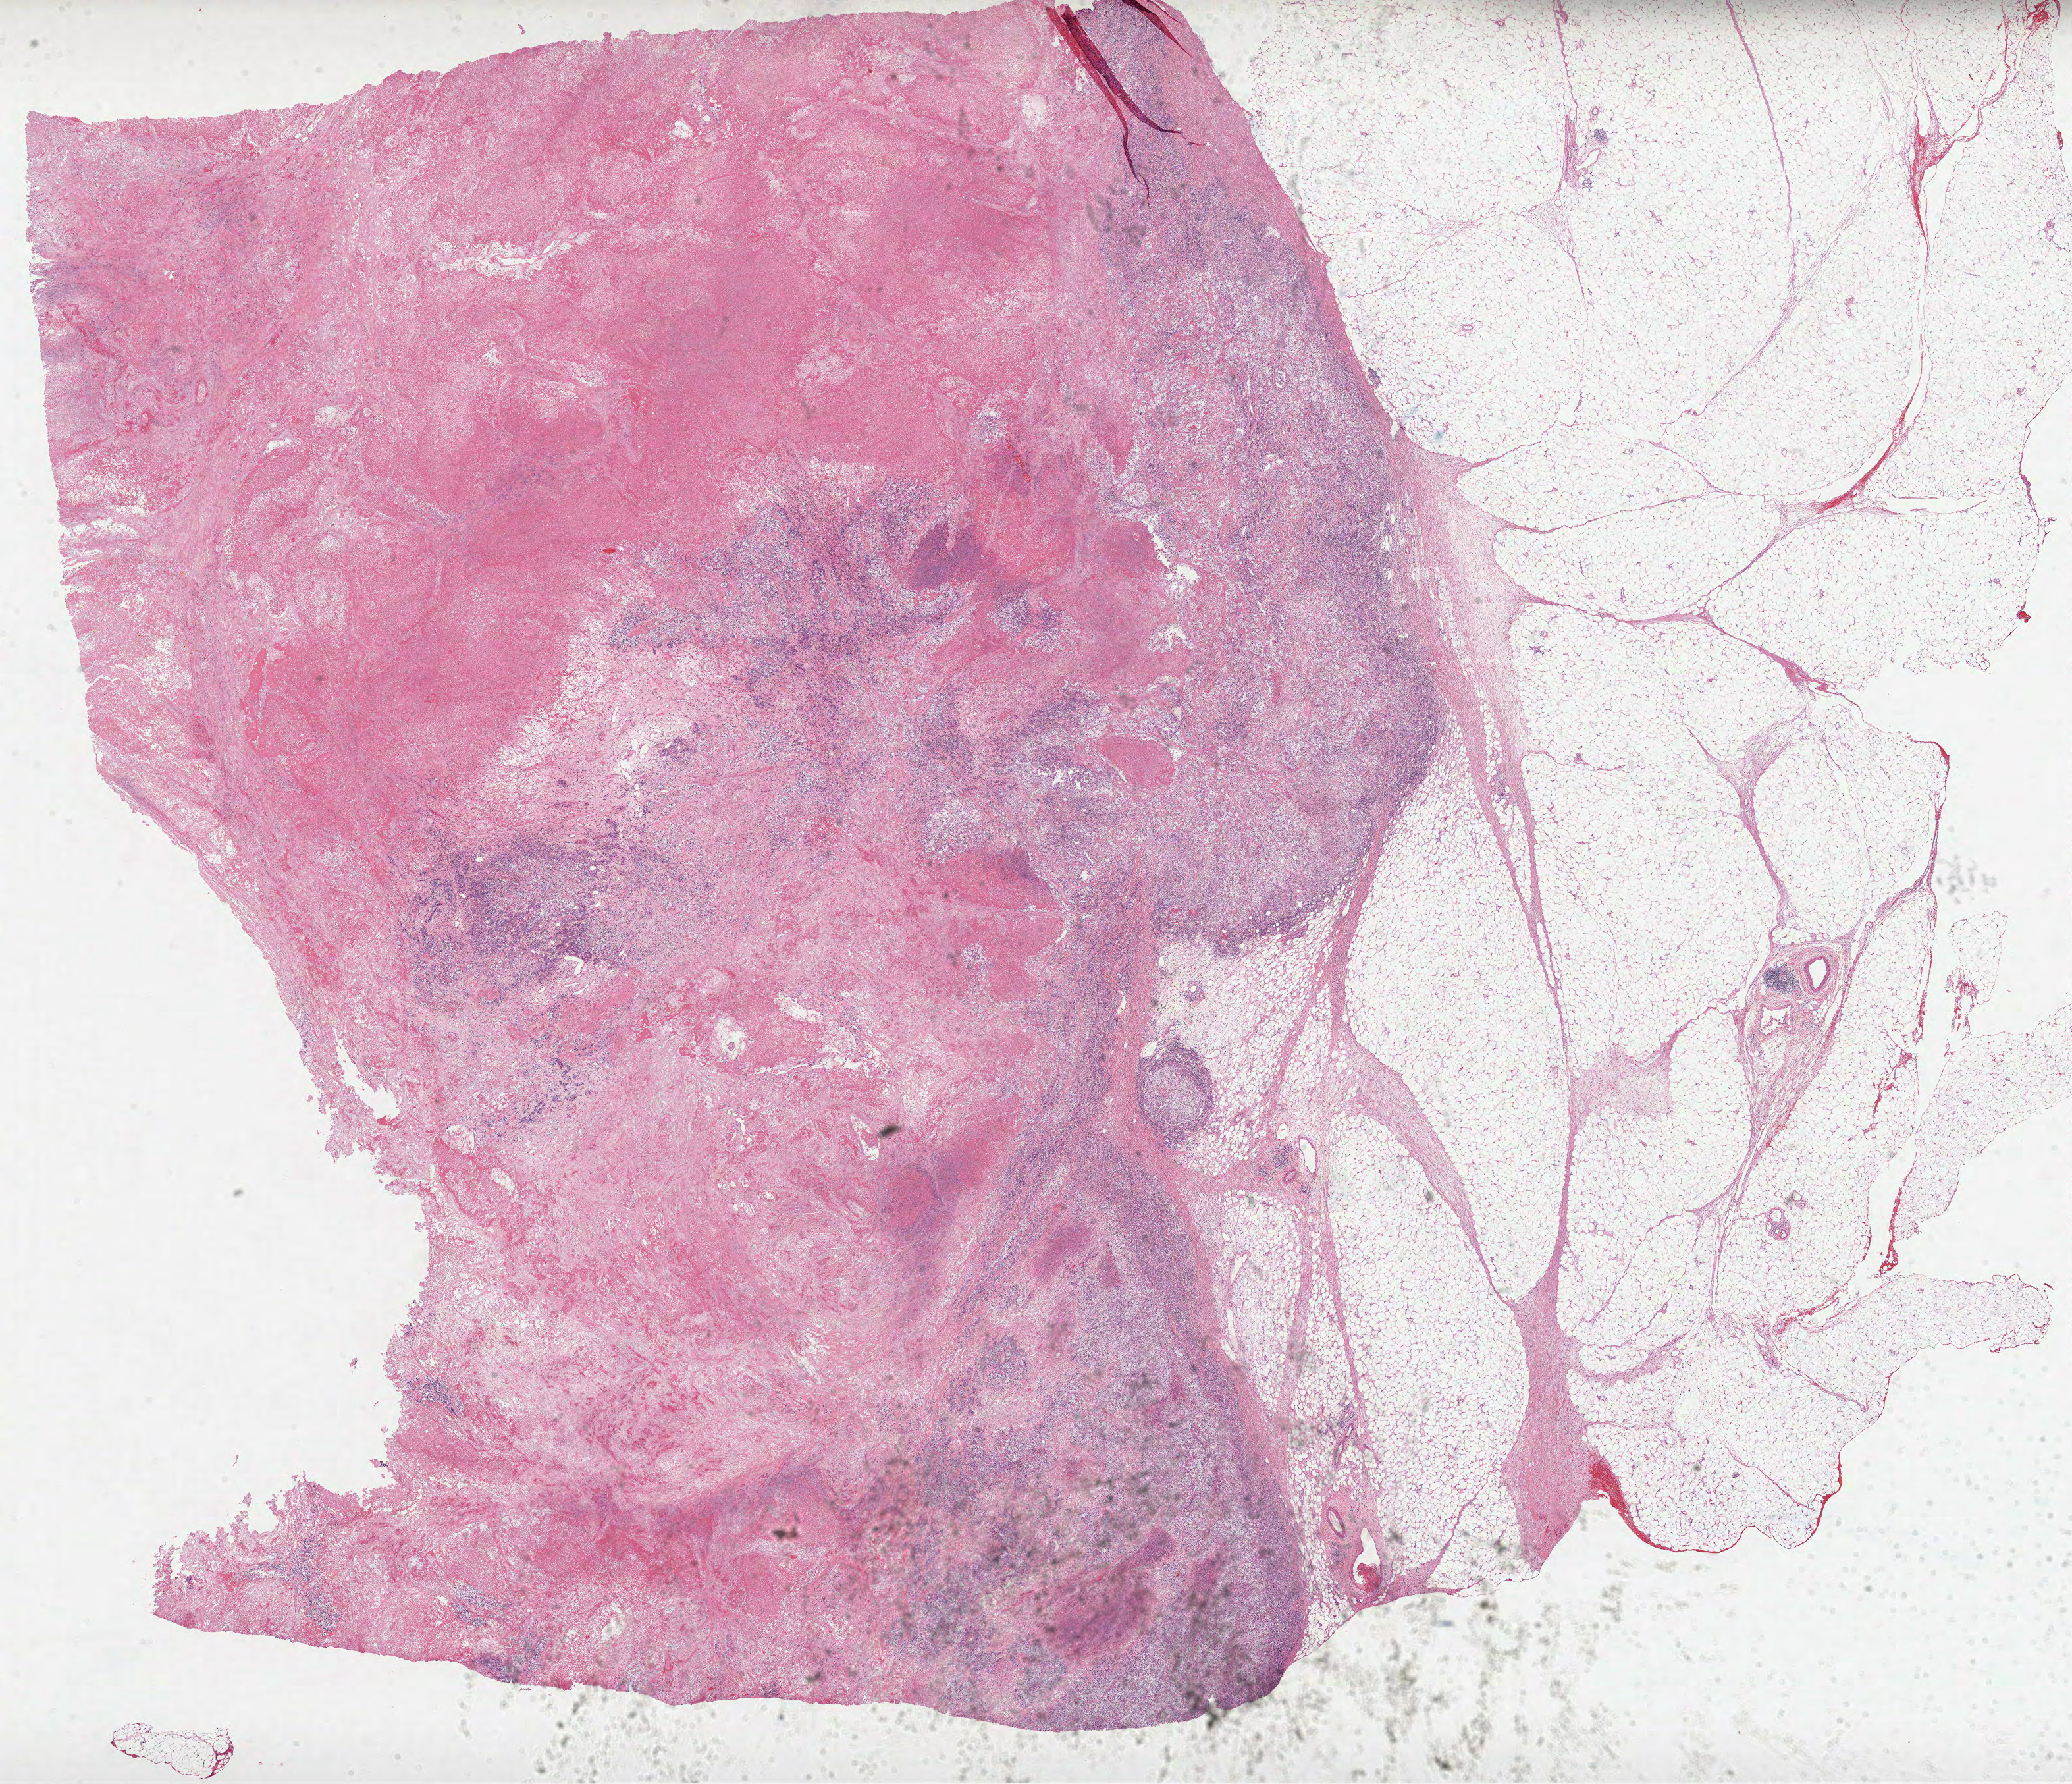
Whole-slide histology image, Hematoxylin and eosin (H&E) stained, whole scanned area (about 25.4 x 21.8 mm) shown as a low-resolution overview. Formalin-fixed paraffin-embedded (FFPE) diagnostic section. Sample: primary tumour, kidney. Male, age 69 years at initial diagnosis. Histologic grade: G4 (undifferentiated).
Pathologic diagnosis: Clear cell adenocarcinoma, NOS. AJCC pathologic stage: III. Lymph nodes positive (case pathology): 1 of 1 examined.